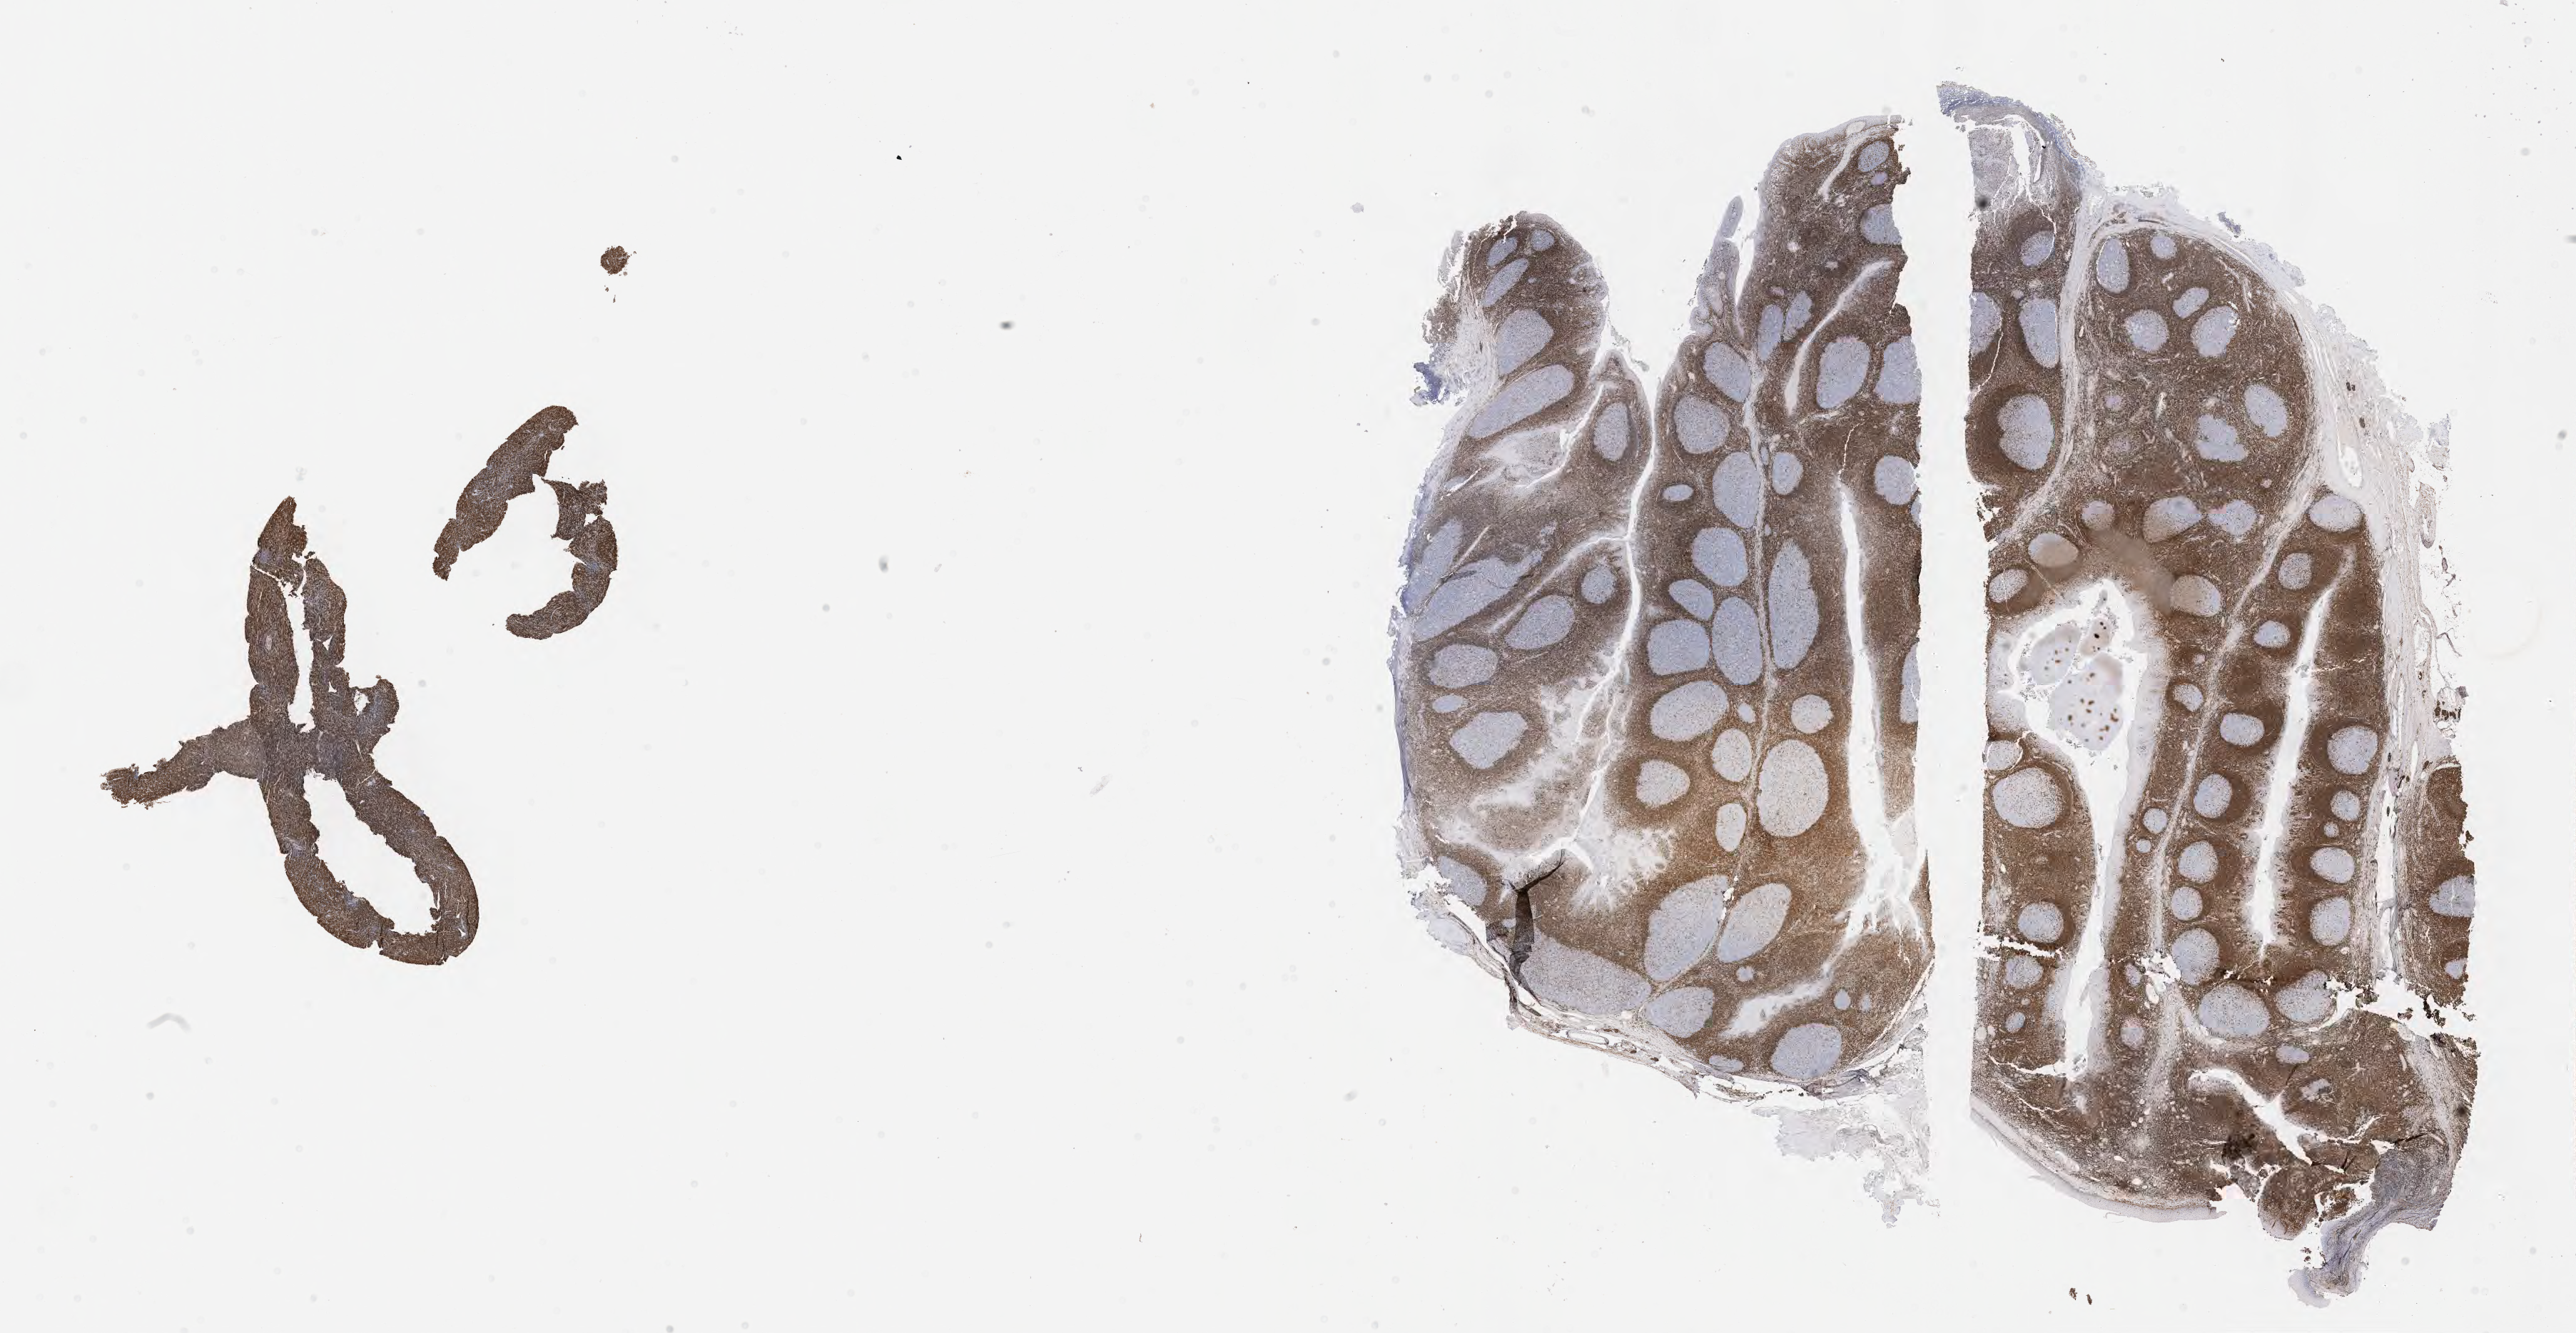
Immunohistochemistry (IHC) whole-slide image stained for BCL2 — whole scanned area (about 29.2 x 15.1 mm) shown as a low-resolution overview. Patient male; age 52 years.
* specimen: tumor tissue; site: liver